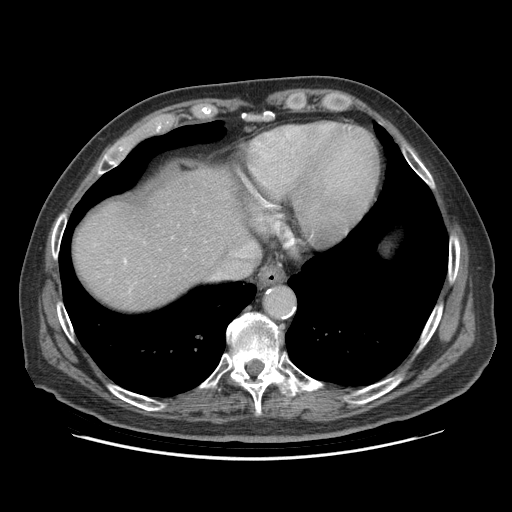
Contrast-enhanced abdominal CT (liver protocol), one axial slice; position 79 of 95 along the scan axis; 140 kVp; soft-tissue window (W 400 / L 40 HU); 512 × 512 image matrix, field of view 400 × 400 mm. From the clinical record (not read from this slice): diagnosis: hepatocellular carcinoma (patient treated with transarterial chemoembolisation; whether this scan precedes or follows treatment is not stated here); TNM stage (as recorded): Stage-IVB; Child-Pugh class: A; tumour differentiation: well differentiated.
Structures marked on this image (semi-automatically segmented with operator editing):
- liver parenchyma outside the tumour (the mass and vessels are separate outlines, so this box may not span the whole liver): bounding box <72,168,248,310> (left, top, right, bottom; pixels)
- liver vessels: <124,259,127,263>